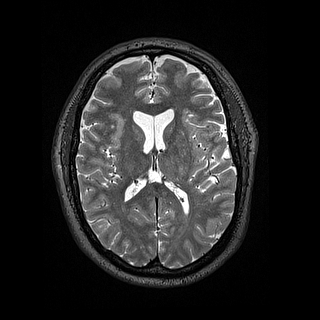
Brain MRI from a brain-tumour surgery series, one axial slice. Position 75 of 144 along the scan axis. 1.2 mm slice thickness. 320 × 320 image matrix, field of view 254 × 254 mm. Case-level facts recorded for this patient, not image findings: histopathology: Astrocytoma; WHO grade: 2; IDH mutation: yes; tumour location: Left Insular.
Annotated regions visible in this slice (manually delineated by an expert):
- tumour: bounding box (x1, y1, x2, y2) in pixels: (195, 156, 208, 169)